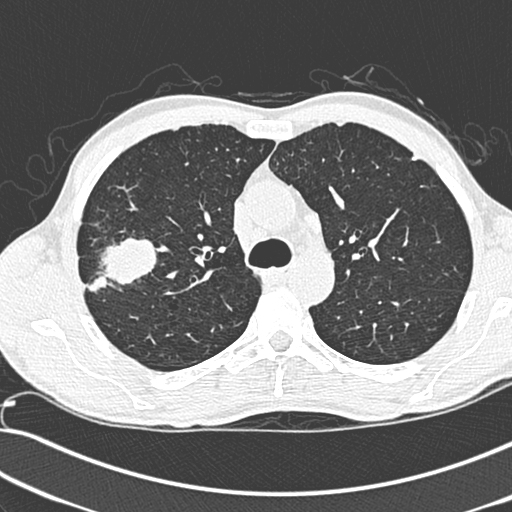
Low-dose screening chest CT, one axial slice; position 207 of 281 along the scan axis; lung window (W 1500 / L -600 HU); 1.3 mm slice thickness; 512 × 512 image matrix.
Outlined on this slice (expert manual segmentation):
- lesion 1 (tumor, upper lobe of right lung): bounding box <87,237,159,301> (left, top, right, bottom; pixels)